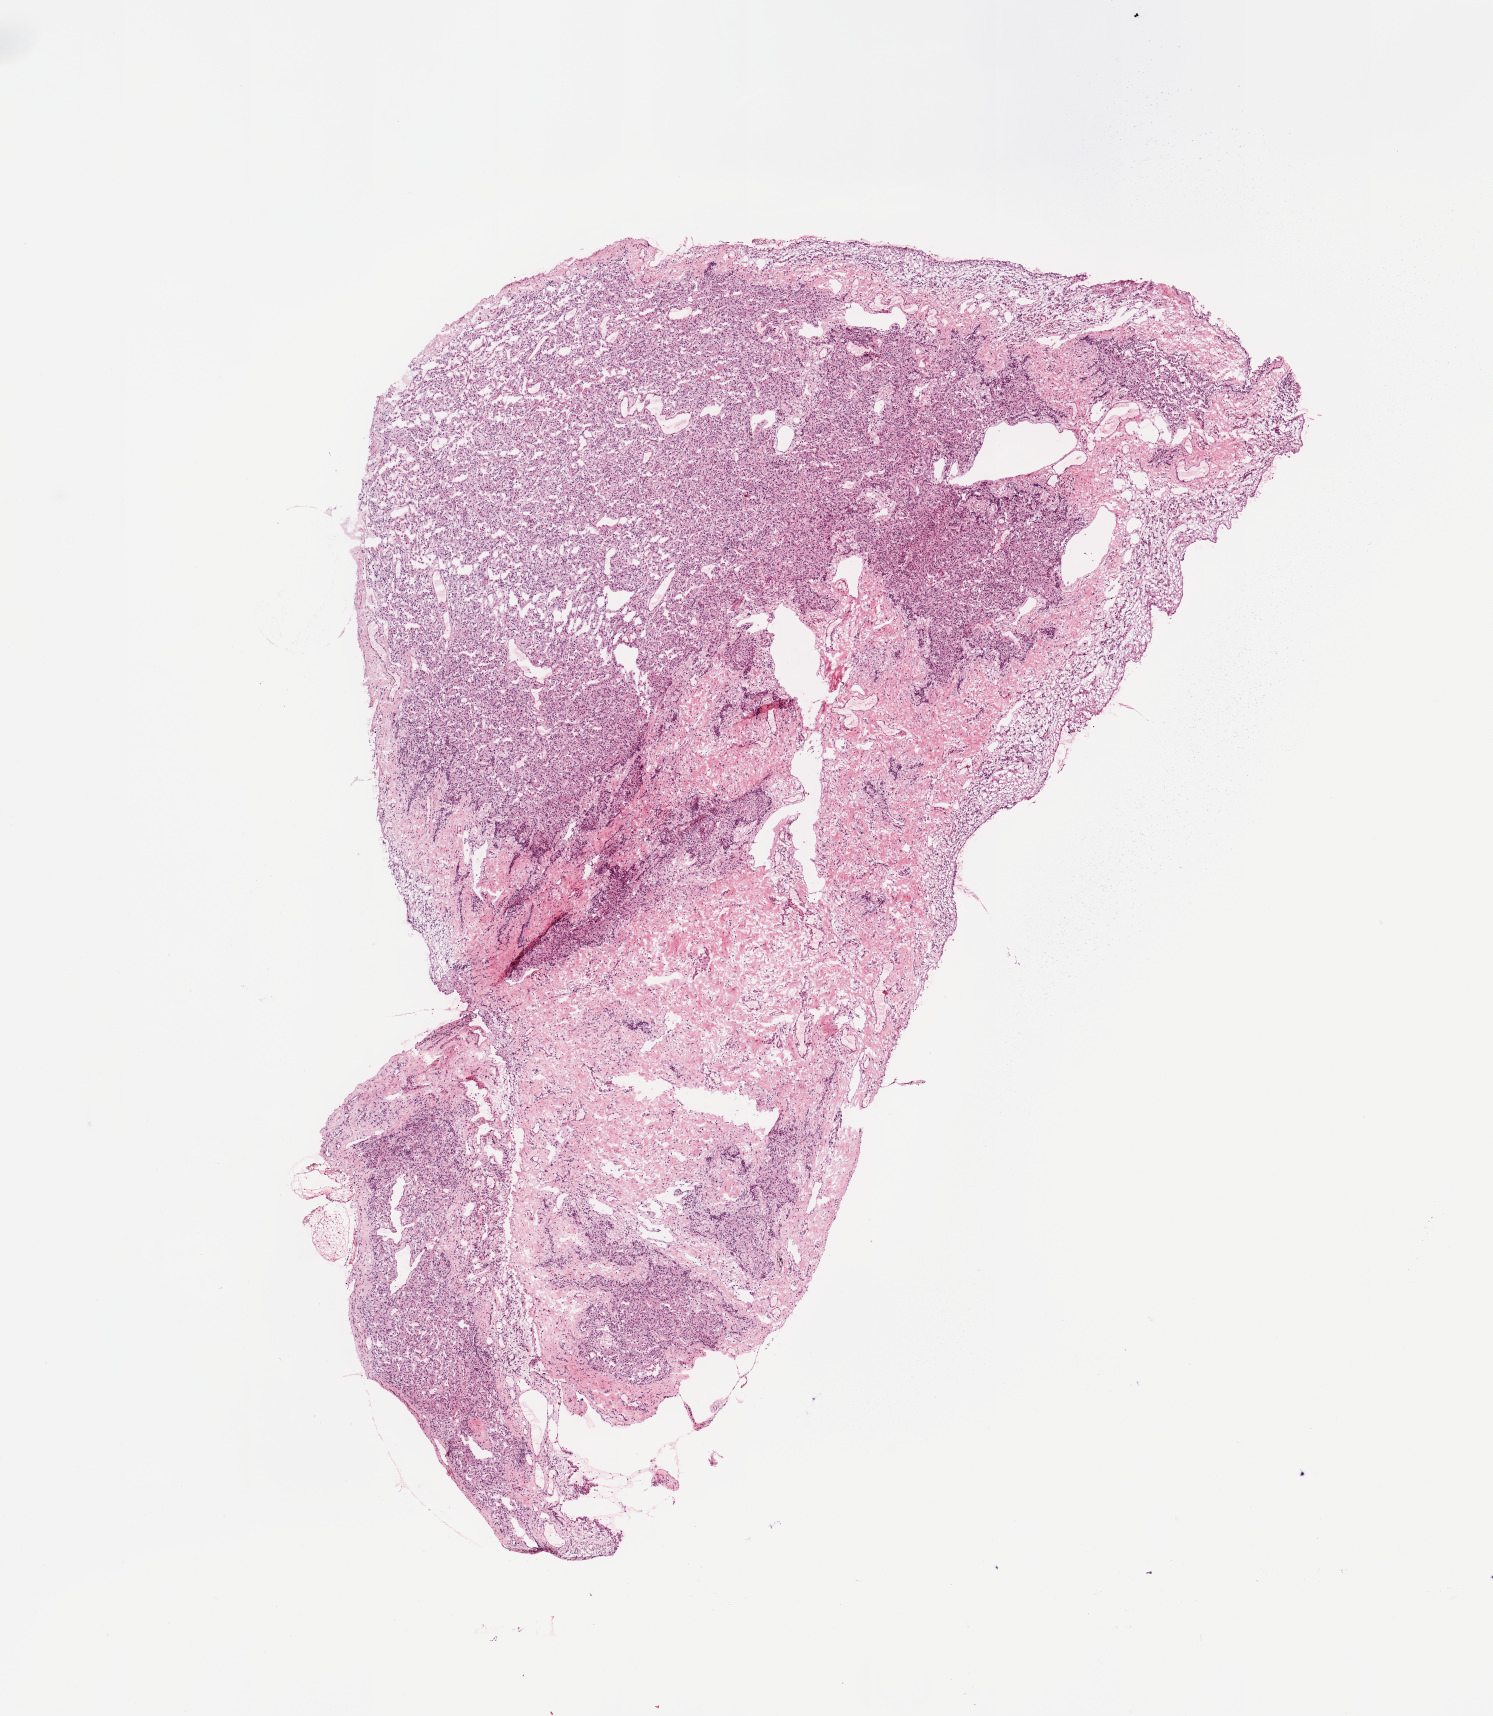
Whole-slide histology image, Hematoxylin and eosin (H&E) stained — low-resolution overview of the scanned area, about 11.8 x 13.6 mm (slide scanned at 20x); lung, normal (non-tumour) tissue. 35-year-old female patient.
This section: normal (non-tumour) tissue from the same patient. Patient diagnosis: Adenocarcinoma, NOS.